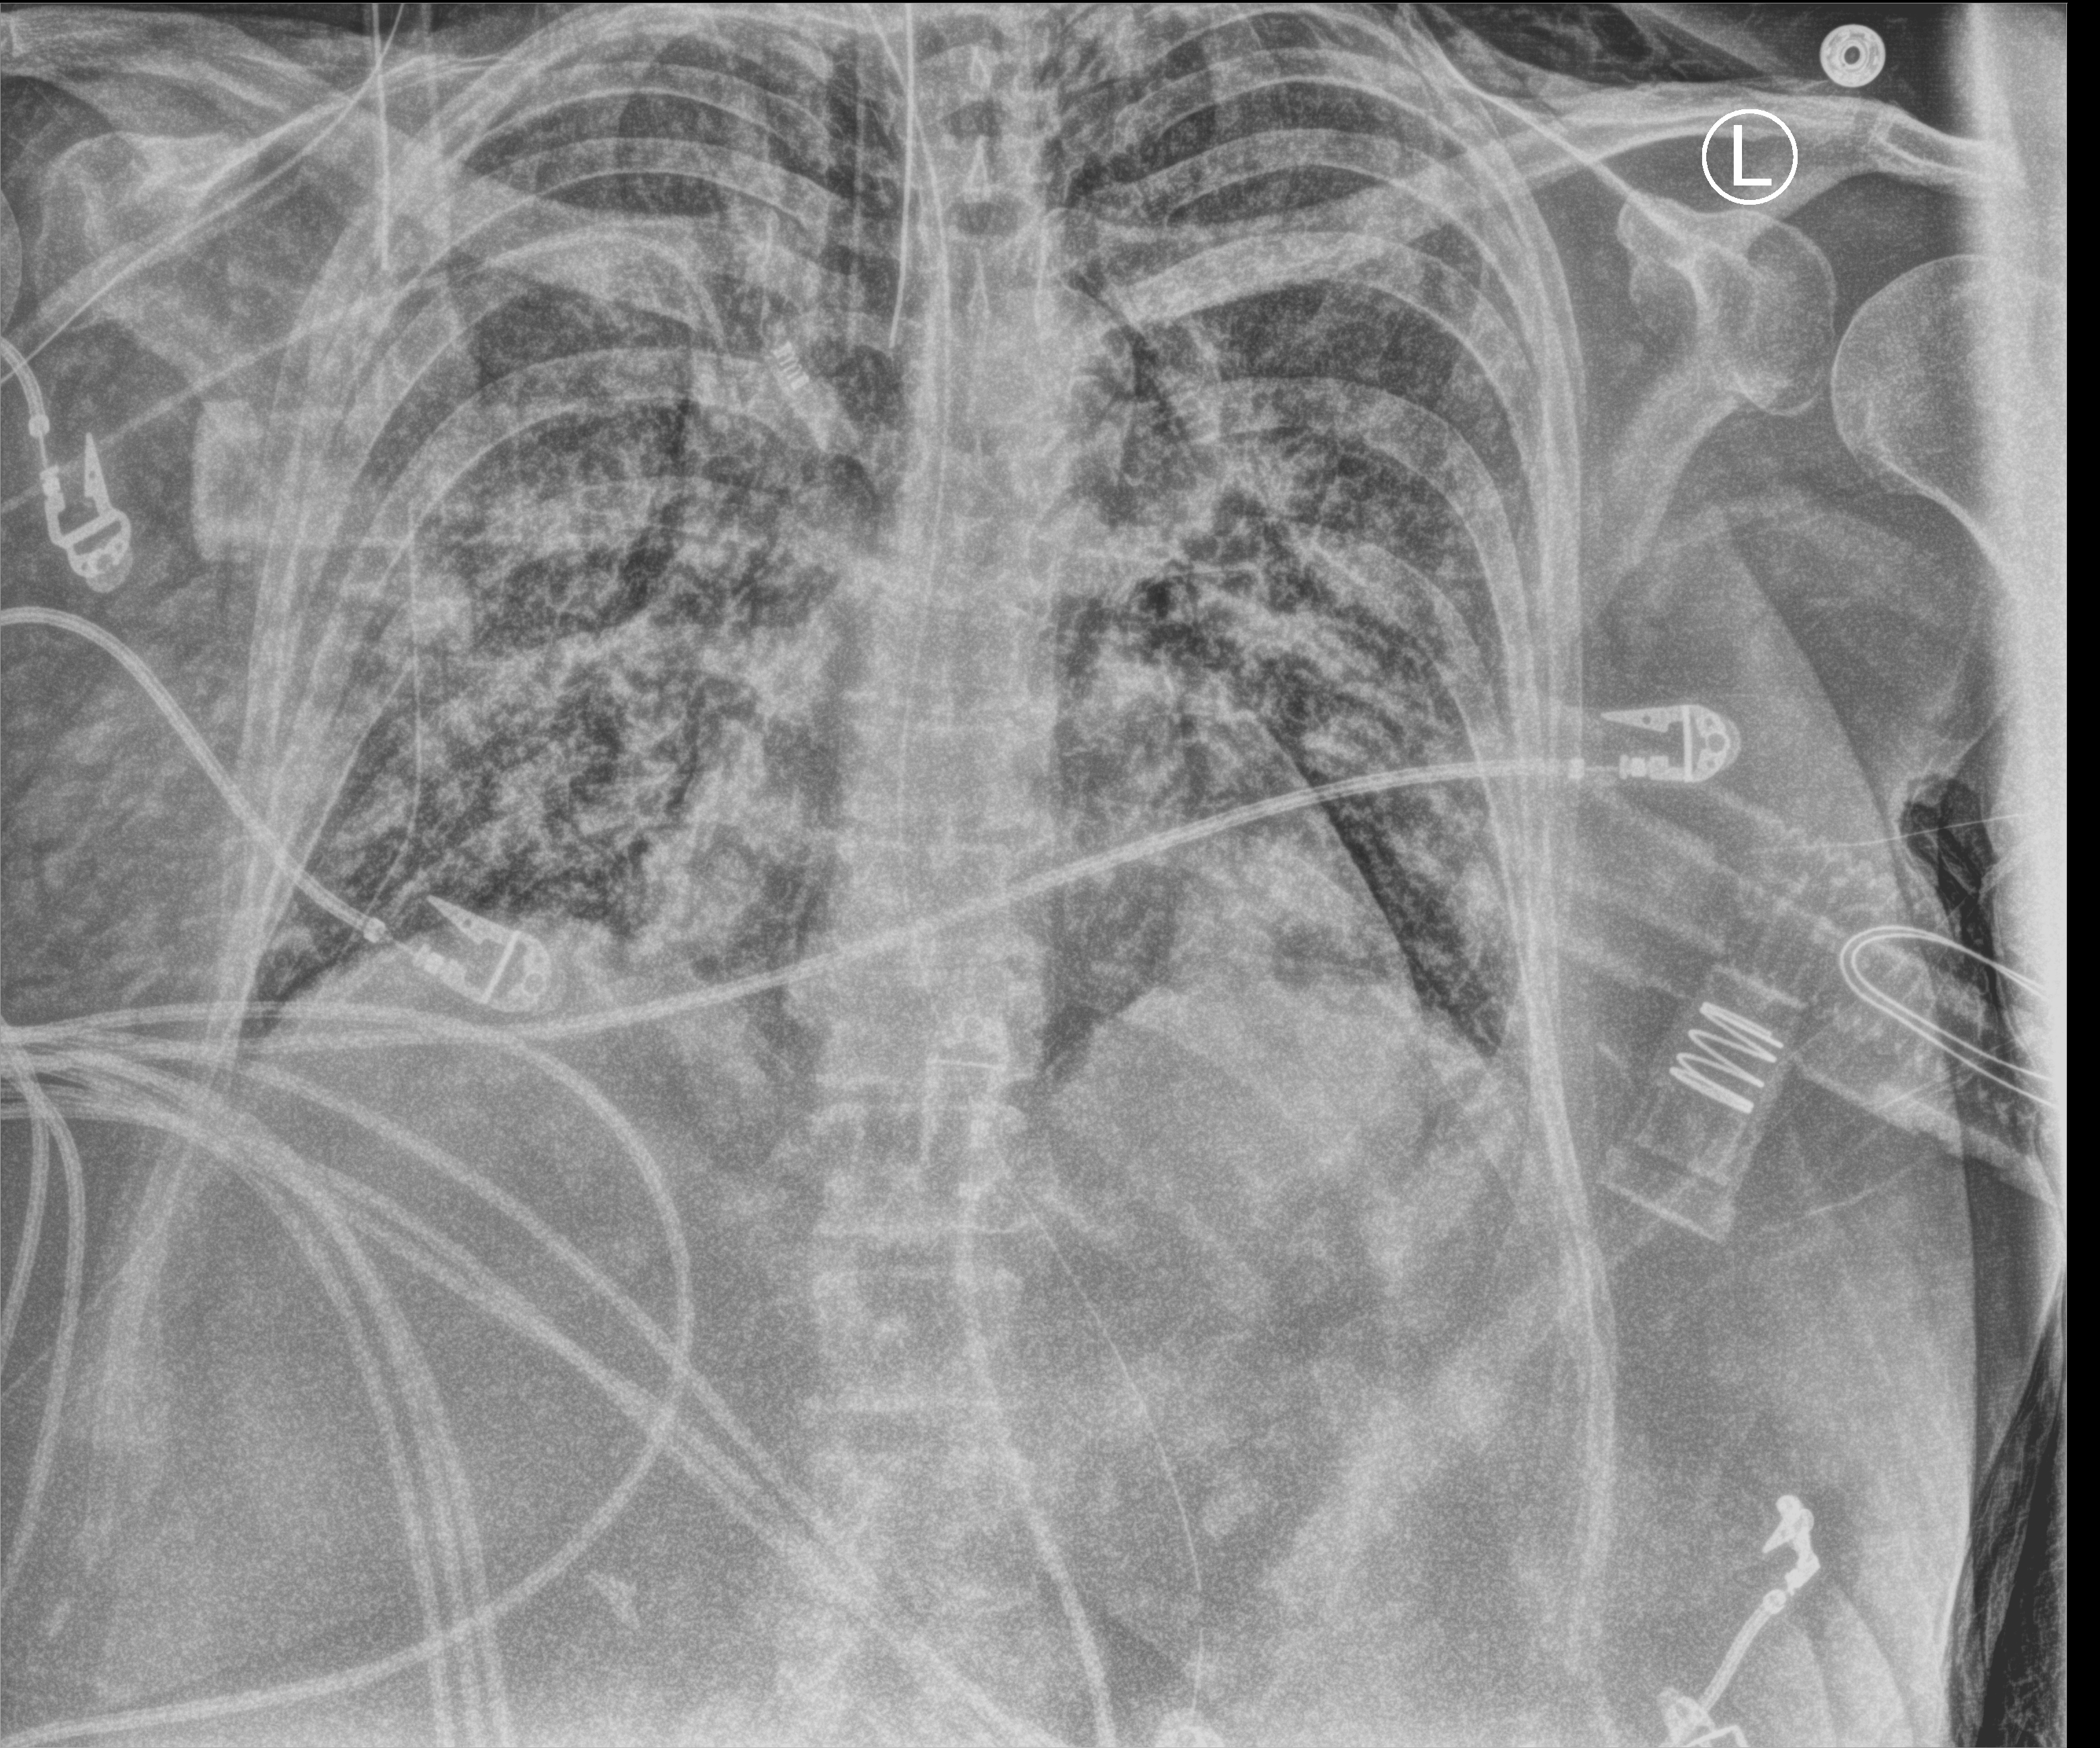
Portable chest radiograph; anteroposterior (AP) projection. Female patient hospitalised with COVID-19, age 60–74 years.
Admission-level facts for this patient (not findings on this image; timing relative to this image not recorded): hypertension (admission record): yes; admitted to intensive care during this hospital stay: yes; length of hospital stay: 45 days.